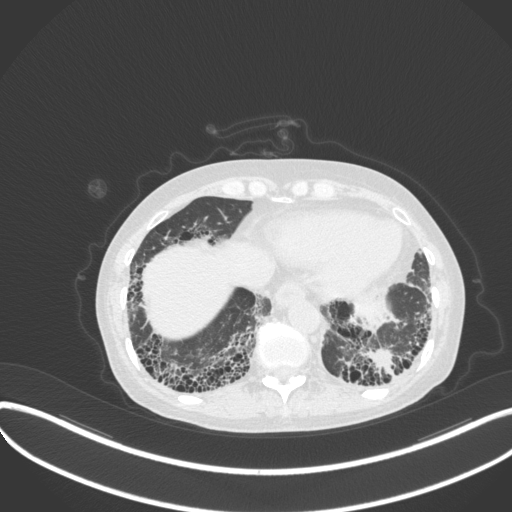
Chest CT, one axial slice; slice 66 of 373 in the series (ordered by position); reconstruction kernel B31f; lung window (W 1500 / L -600 HU); 512 × 512 image matrix. Female patient, age 56 years. Case-level facts recorded for this patient, not image findings: clinical TNM (as recorded): T1 N0 M0.
Structures marked on this image (bounding box drawn by a radiologist):
- lung tumour (recorded histology: adenocarcinoma): bounding box (x1, y1, x2, y2) in pixels: (365, 346, 391, 378)